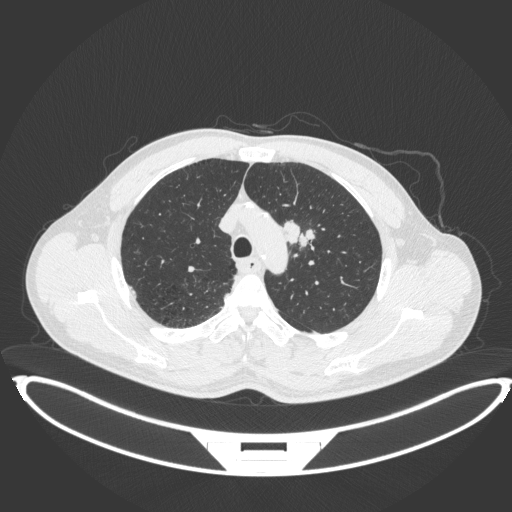
Chest CT, one axial slice. Position 333 of 407 along the scan axis. Reconstruction kernel B31f. 120 kVp. Lung window (W 1500 / L -600 HU). 1 mm slice thickness. 512 × 512 image matrix, field of view 457 × 457 mm. Male patient, age 60 years. Case-level facts recorded for this patient, not image findings: clinical TNM (as recorded): T2a N0 M0; histopathological grade: G1-G2.
Structures marked on this image (bounding box drawn by a radiologist):
- lung tumour (recorded histology: squamous cell carcinoma): bounding box <281,218,318,250> (left, top, right, bottom; pixels)